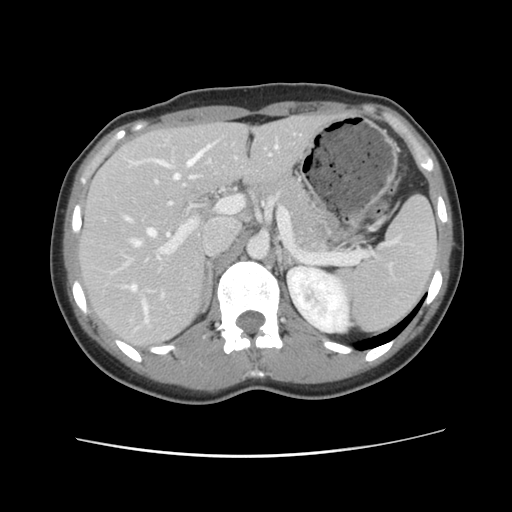
Contrast-enhanced abdominal CT, one axial slice. Position 66 of 134 along the scan axis. 120 kVp. Intravenous contrast given. Soft-tissue window (W 400 / L 40 HU). 512 × 512 image matrix, field of view 339 × 339 mm. Female patient, age 33 years. From the clinical record (not read from this slice): diagnosis: colorectal cancer liver metastases, imaged before liver resection; multiple liver metastases: yes; largest metastasis: 4.5 cm.
Outlined on this slice (manually delineated by an expert):
- hepatic veins: bounding box (x1, y1, x2, y2) in pixels: (125, 144, 278, 323)
- liver: (80, 115, 327, 349)
- planned liver remnant (the part of the liver to remain after resection): (80, 115, 329, 348)
- portal vein (with intrahepatic branches): (110, 183, 235, 300)